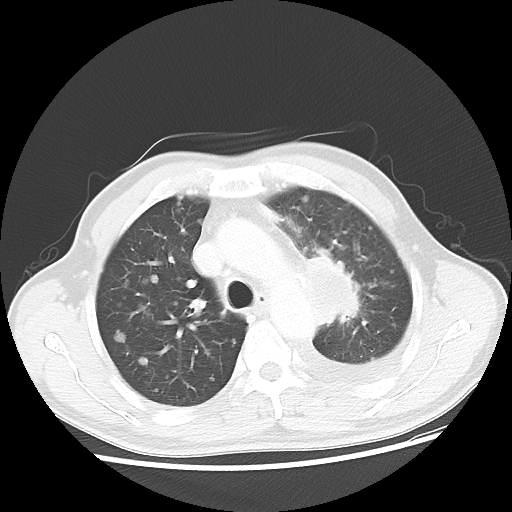
Chest CT, one axial slice. Position 33 of 47 along the scan axis. Reconstruction kernel LUNG. 100 kVp. Lung window (W 1500 / L -600 HU). 512 × 512 image matrix, field of view 362 × 362 mm. Patient: male, 55 years. Case-level facts recorded for this patient, not image findings: clinical TNM (as recorded): T2 N3 M1a.
Structures marked on this image (rectangle marked by the reading radiologist):
- lung tumour (recorded histology: squamous cell carcinoma): bounding box (x1, y1, x2, y2) in pixels: (303, 250, 381, 335)